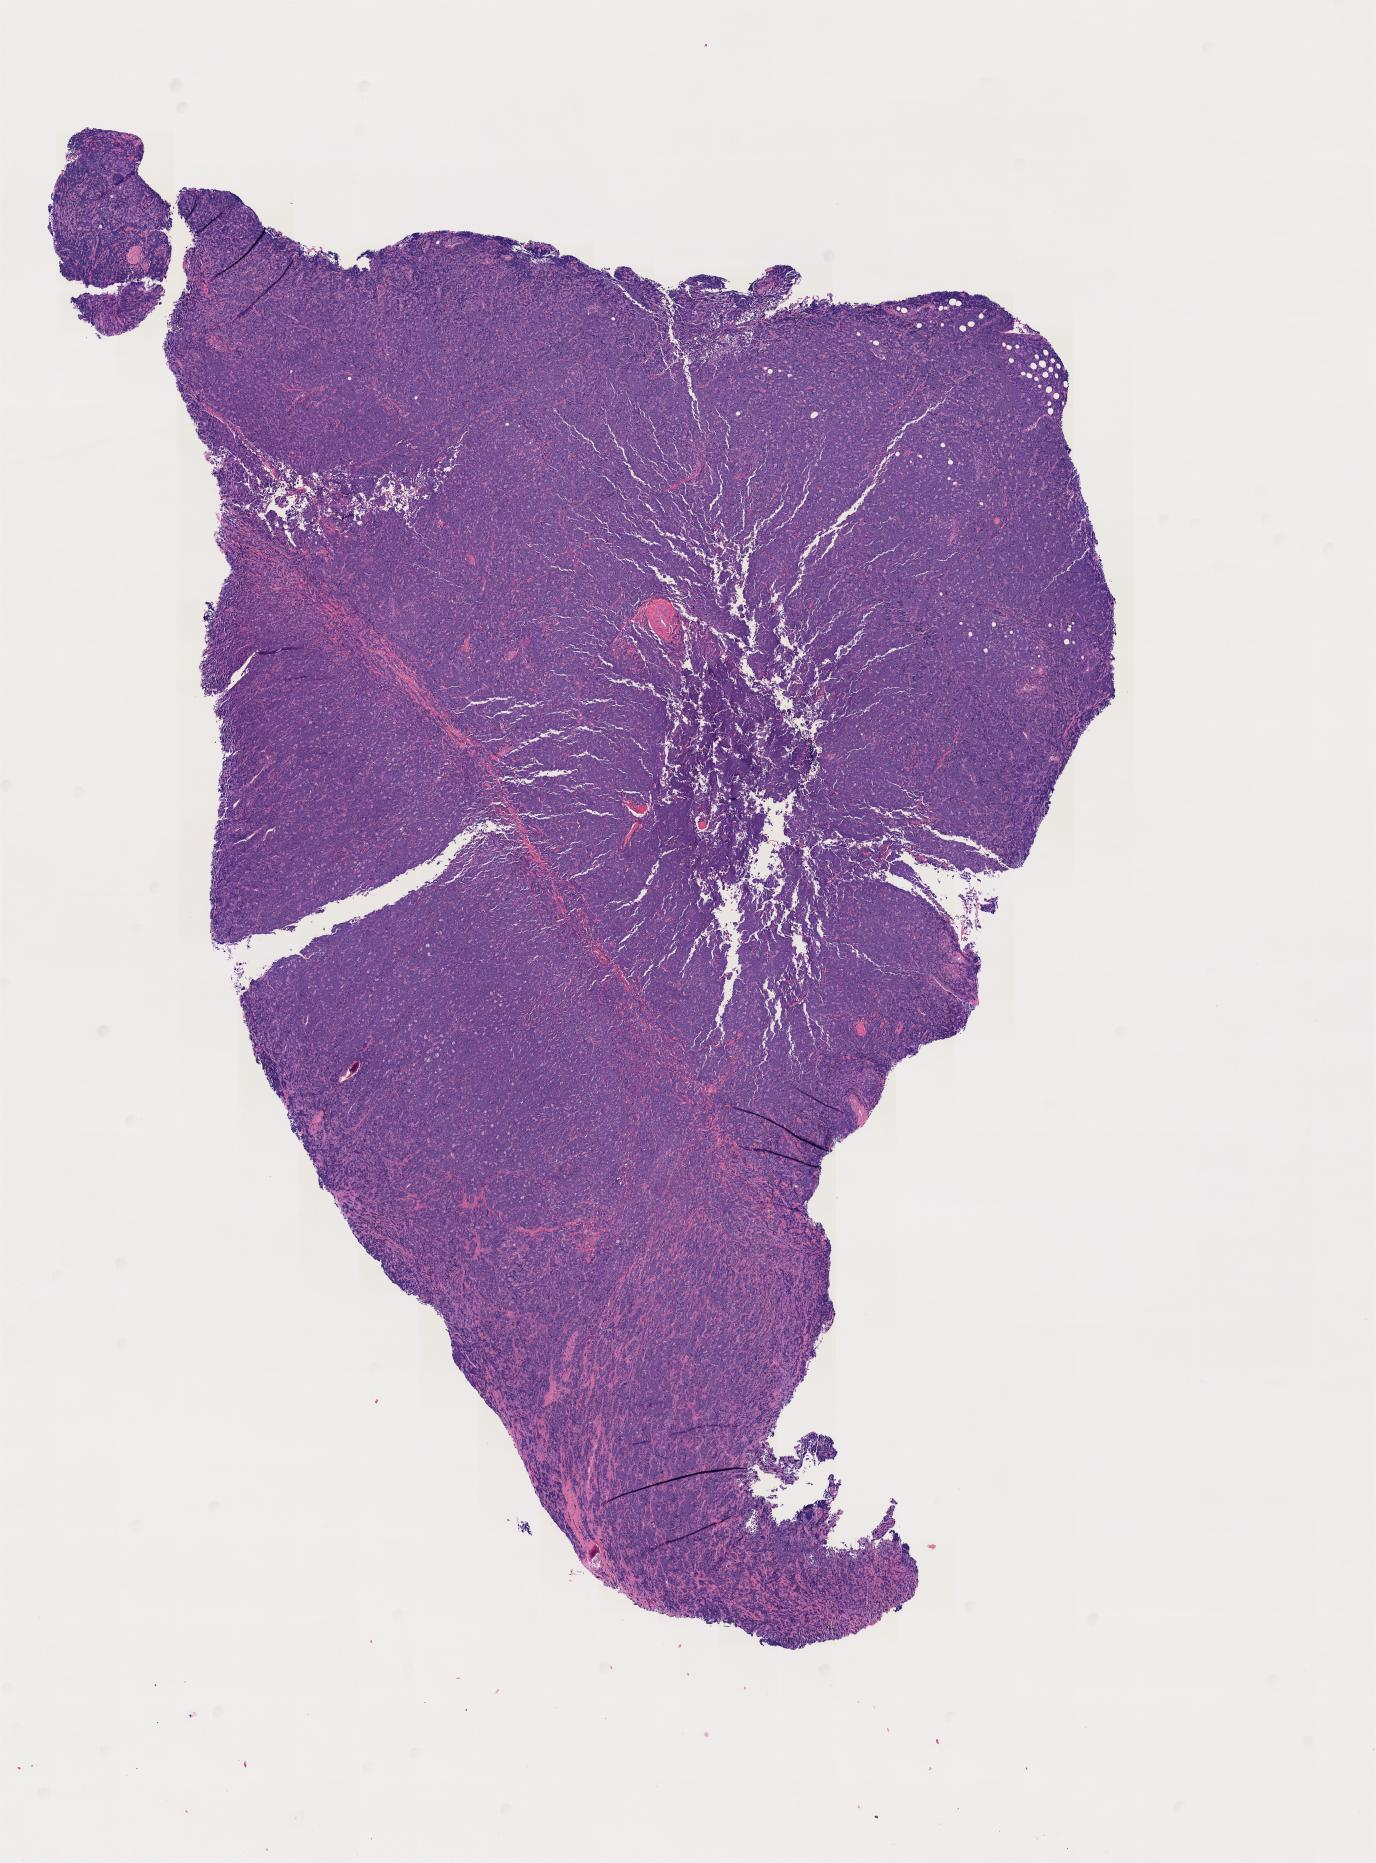
Whole-slide image, H&E stain — low-resolution overview of the scanned area, tumor tissue, site: cranium. Male patient, age 11 years.
Histologic diagnosis: Burkitt lymphoma, NOS.